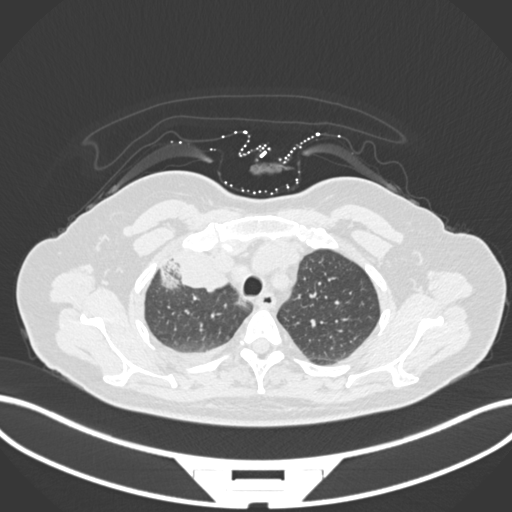
Chest CT, one axial slice. Slice 133 of 172 in the series (ordered by position). Reconstruction kernel B30f. Lung window (W 1500 / L -600 HU). 512 × 512 image matrix, field of view 400 × 400 mm. Patient: female, 52 years. Case-level facts recorded for this patient, not image findings: clinical TNM (as recorded): T3 N1 M1.
Annotated regions visible in this slice (bounding box drawn by a radiologist):
- lung tumour (recorded histology: adenocarcinoma): bounding box [x1, y1, x2, y2] px = [155, 253, 232, 293]